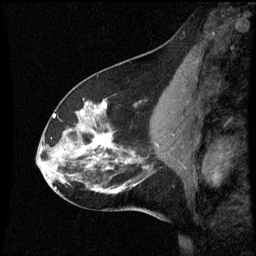
Breast MRI (dynamic contrast-enhanced), one sagittal slice. Slice 28 of 60 in the series (ordered by position). Dynamic contrast-enhanced series, image 2 of 3 at this slice position (ordered by acquisition). 1.5 T. TE 4.2 ms, TR 8.9 ms. 2 mm slice thickness. 256 × 256 image matrix, field of view 200 × 200 mm. Female patient, age 45 years. Case-level facts recorded for this patient, not image findings: setting: breast cancer imaged before/during neoadjuvant chemotherapy; receptor status: HR-positive, HER2-negative.
Structures marked on this image (semi-automatic segmentation, software-assisted and operator-edited):
- analysis volume of interest (the breast-tissue region the enhancement analysis was run in; not a lesion): bounding box (x1, y1, x2, y2) in pixels: (46, 94, 171, 205)
- tumour enhancement mask (voxels above the 70 % enhancement threshold inside the analysis volume of interest): (54, 102, 127, 163)